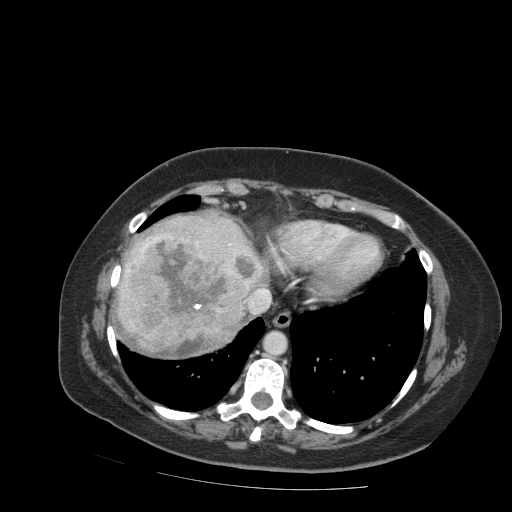
Contrast-enhanced abdominal CT (liver protocol), one axial slice. Slice 78 of 99 in the series (ordered by position). 140 kVp. Soft-tissue window (W 400 / L 40 HU). 512 × 512 image matrix, field of view 400 × 400 mm. From the clinical record (not read from this slice): diagnosis: hepatocellular carcinoma (patient treated with transarterial chemoembolisation; whether this scan precedes or follows treatment is not stated here); TNM stage (as recorded): Stage-IVB; Child-Pugh class: A; tumour differentiation: moderately differentiated; tumour nodularity: uninodular.
Annotated regions visible in this slice (semi-automatically segmented with operator editing):
- liver parenchyma outside the tumour (the mass and vessels are separate outlines, so this box may not span the whole liver): bounding box (x1, y1, x2, y2) in pixels: (116, 214, 266, 342)
- mass: (113, 235, 256, 359)
- liver vessels: (206, 231, 260, 269)